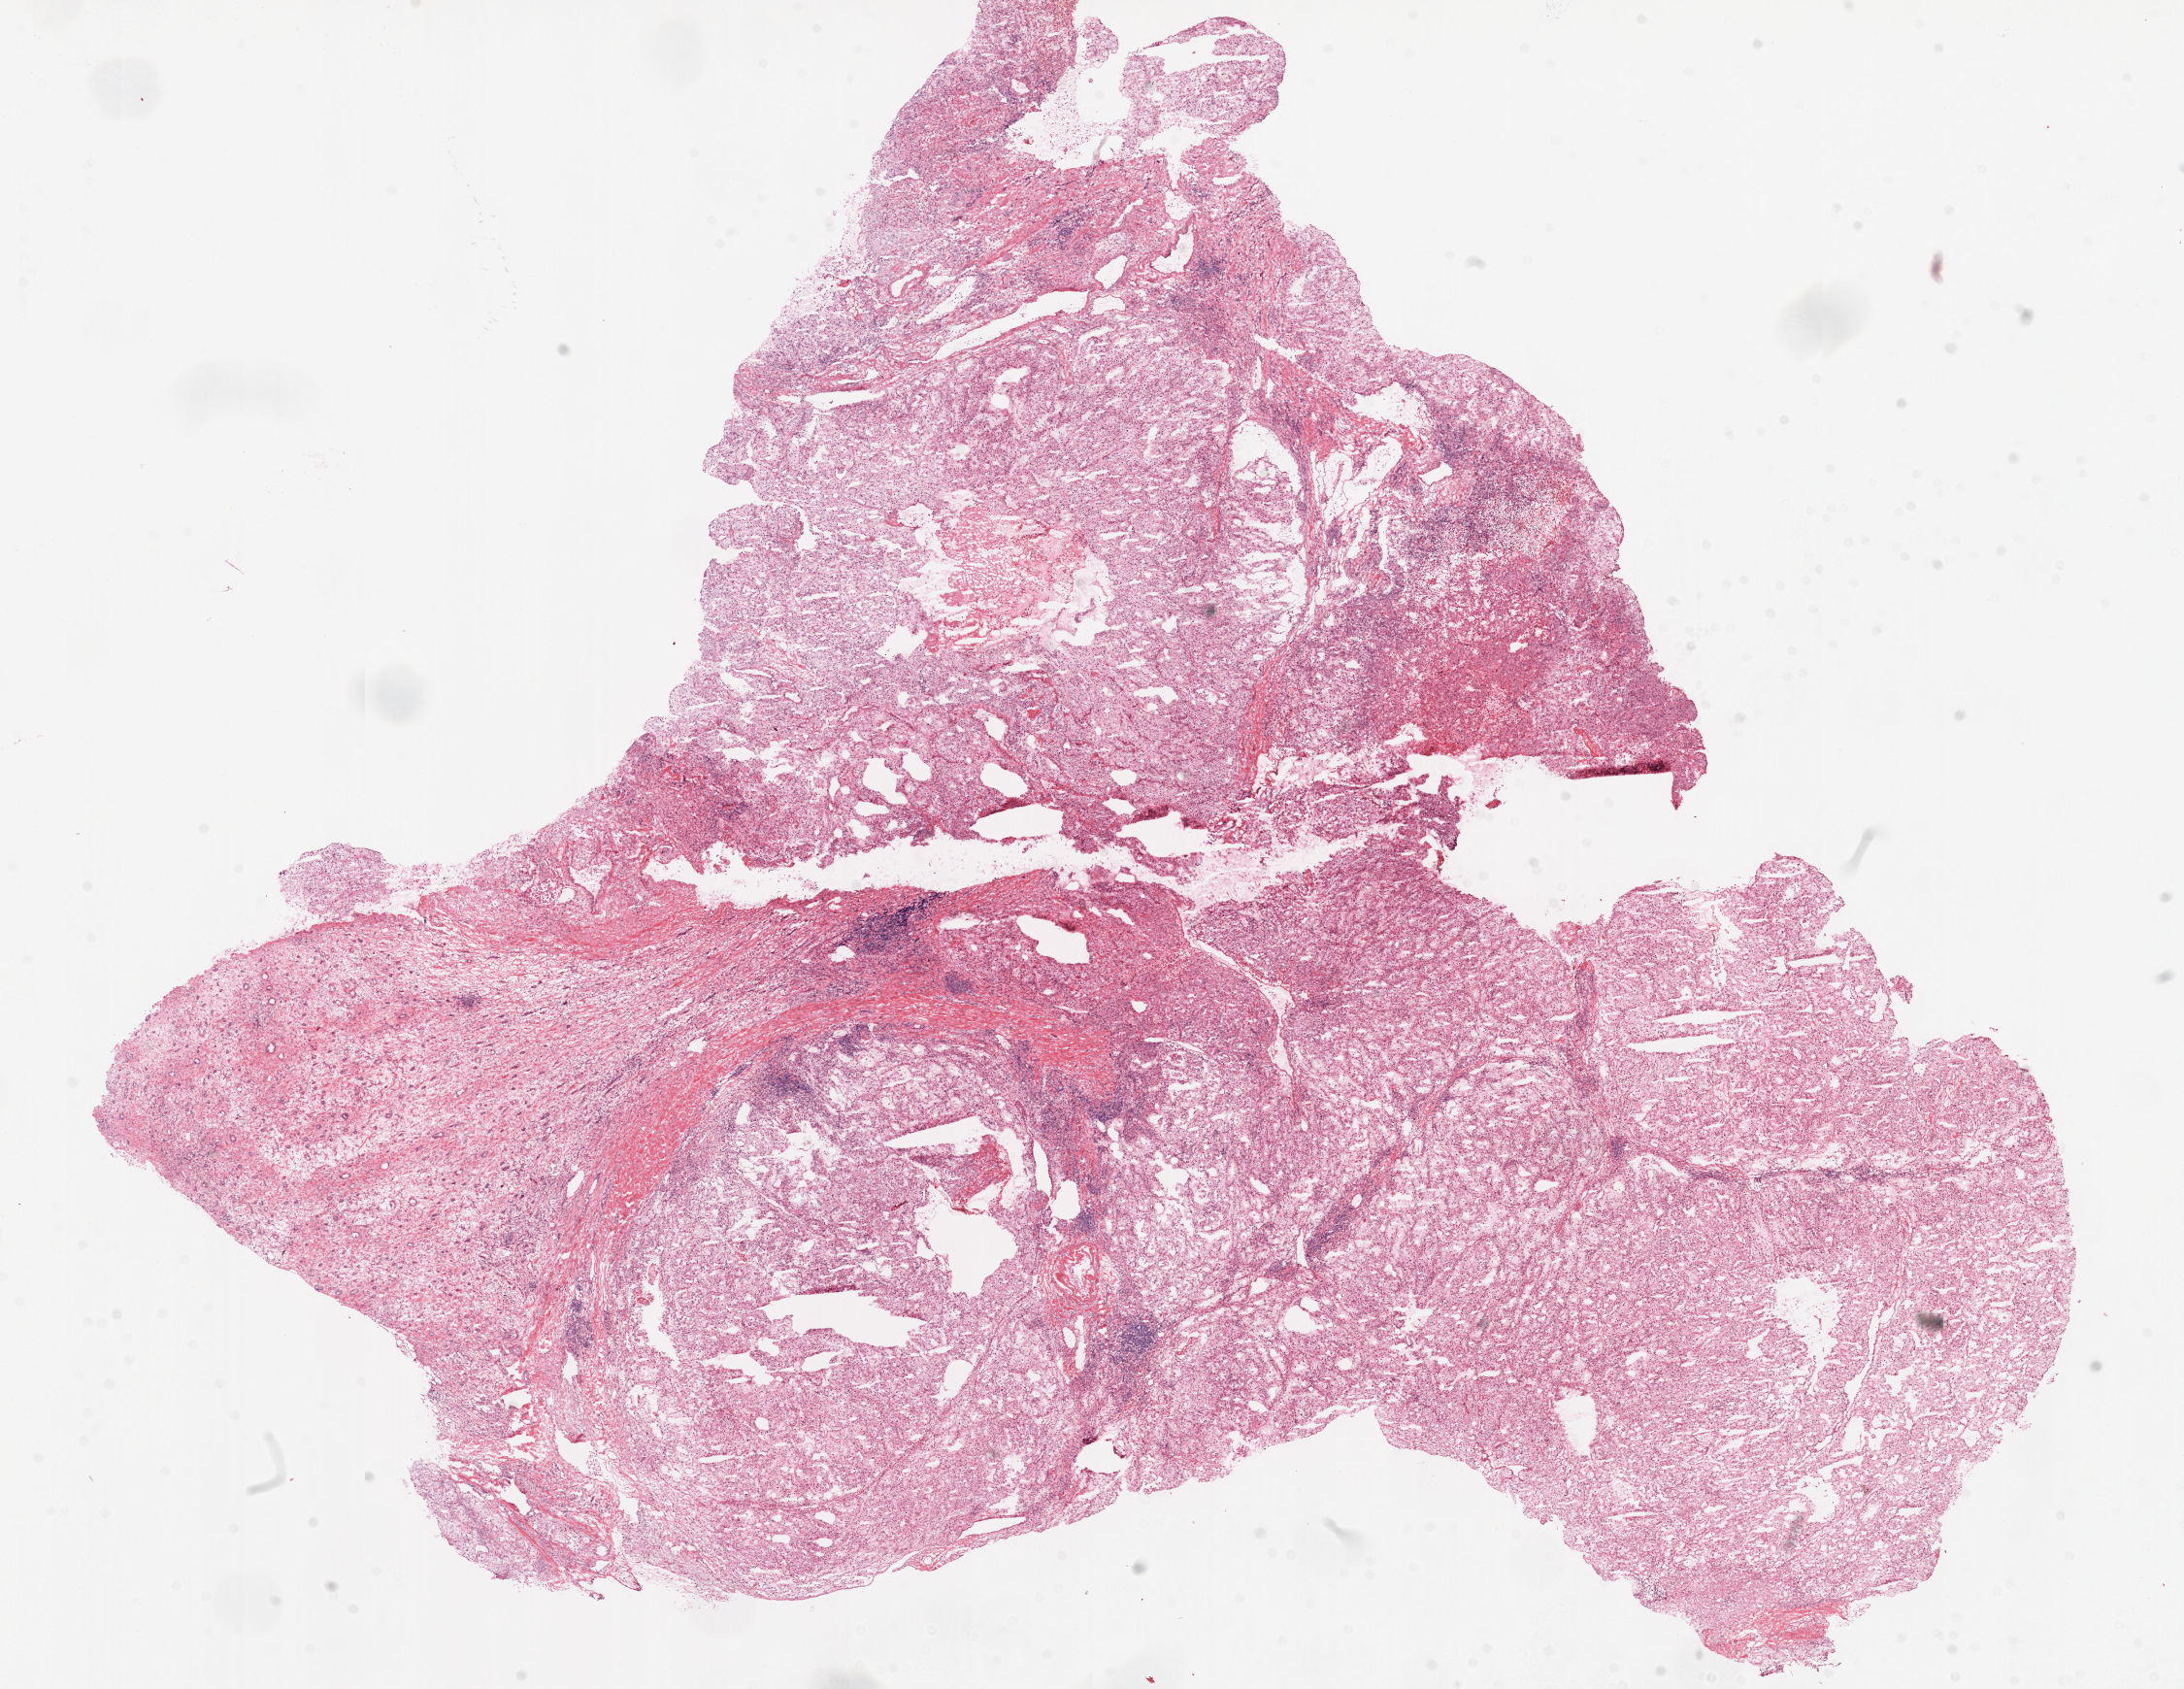
Digitized H&E-stained tissue section (whole slide), a low-resolution overview of the entire scanned area, about 18.1 x 14.0 mm; frozen section; sample: primary tumour, kidney. Male patient; age at initial diagnosis 67 years. Histologic grade: G2 (moderately differentiated). Slide review estimates, as recorded: tumour cells 75%, tumour nuclei 75%, normal cells 15%, stromal cells 10%, necrosis 0%.
• histologic diagnosis: Clear cell adenocarcinoma, NOS
• AJCC pathologic stage: III (6th edition)
• laterality: right